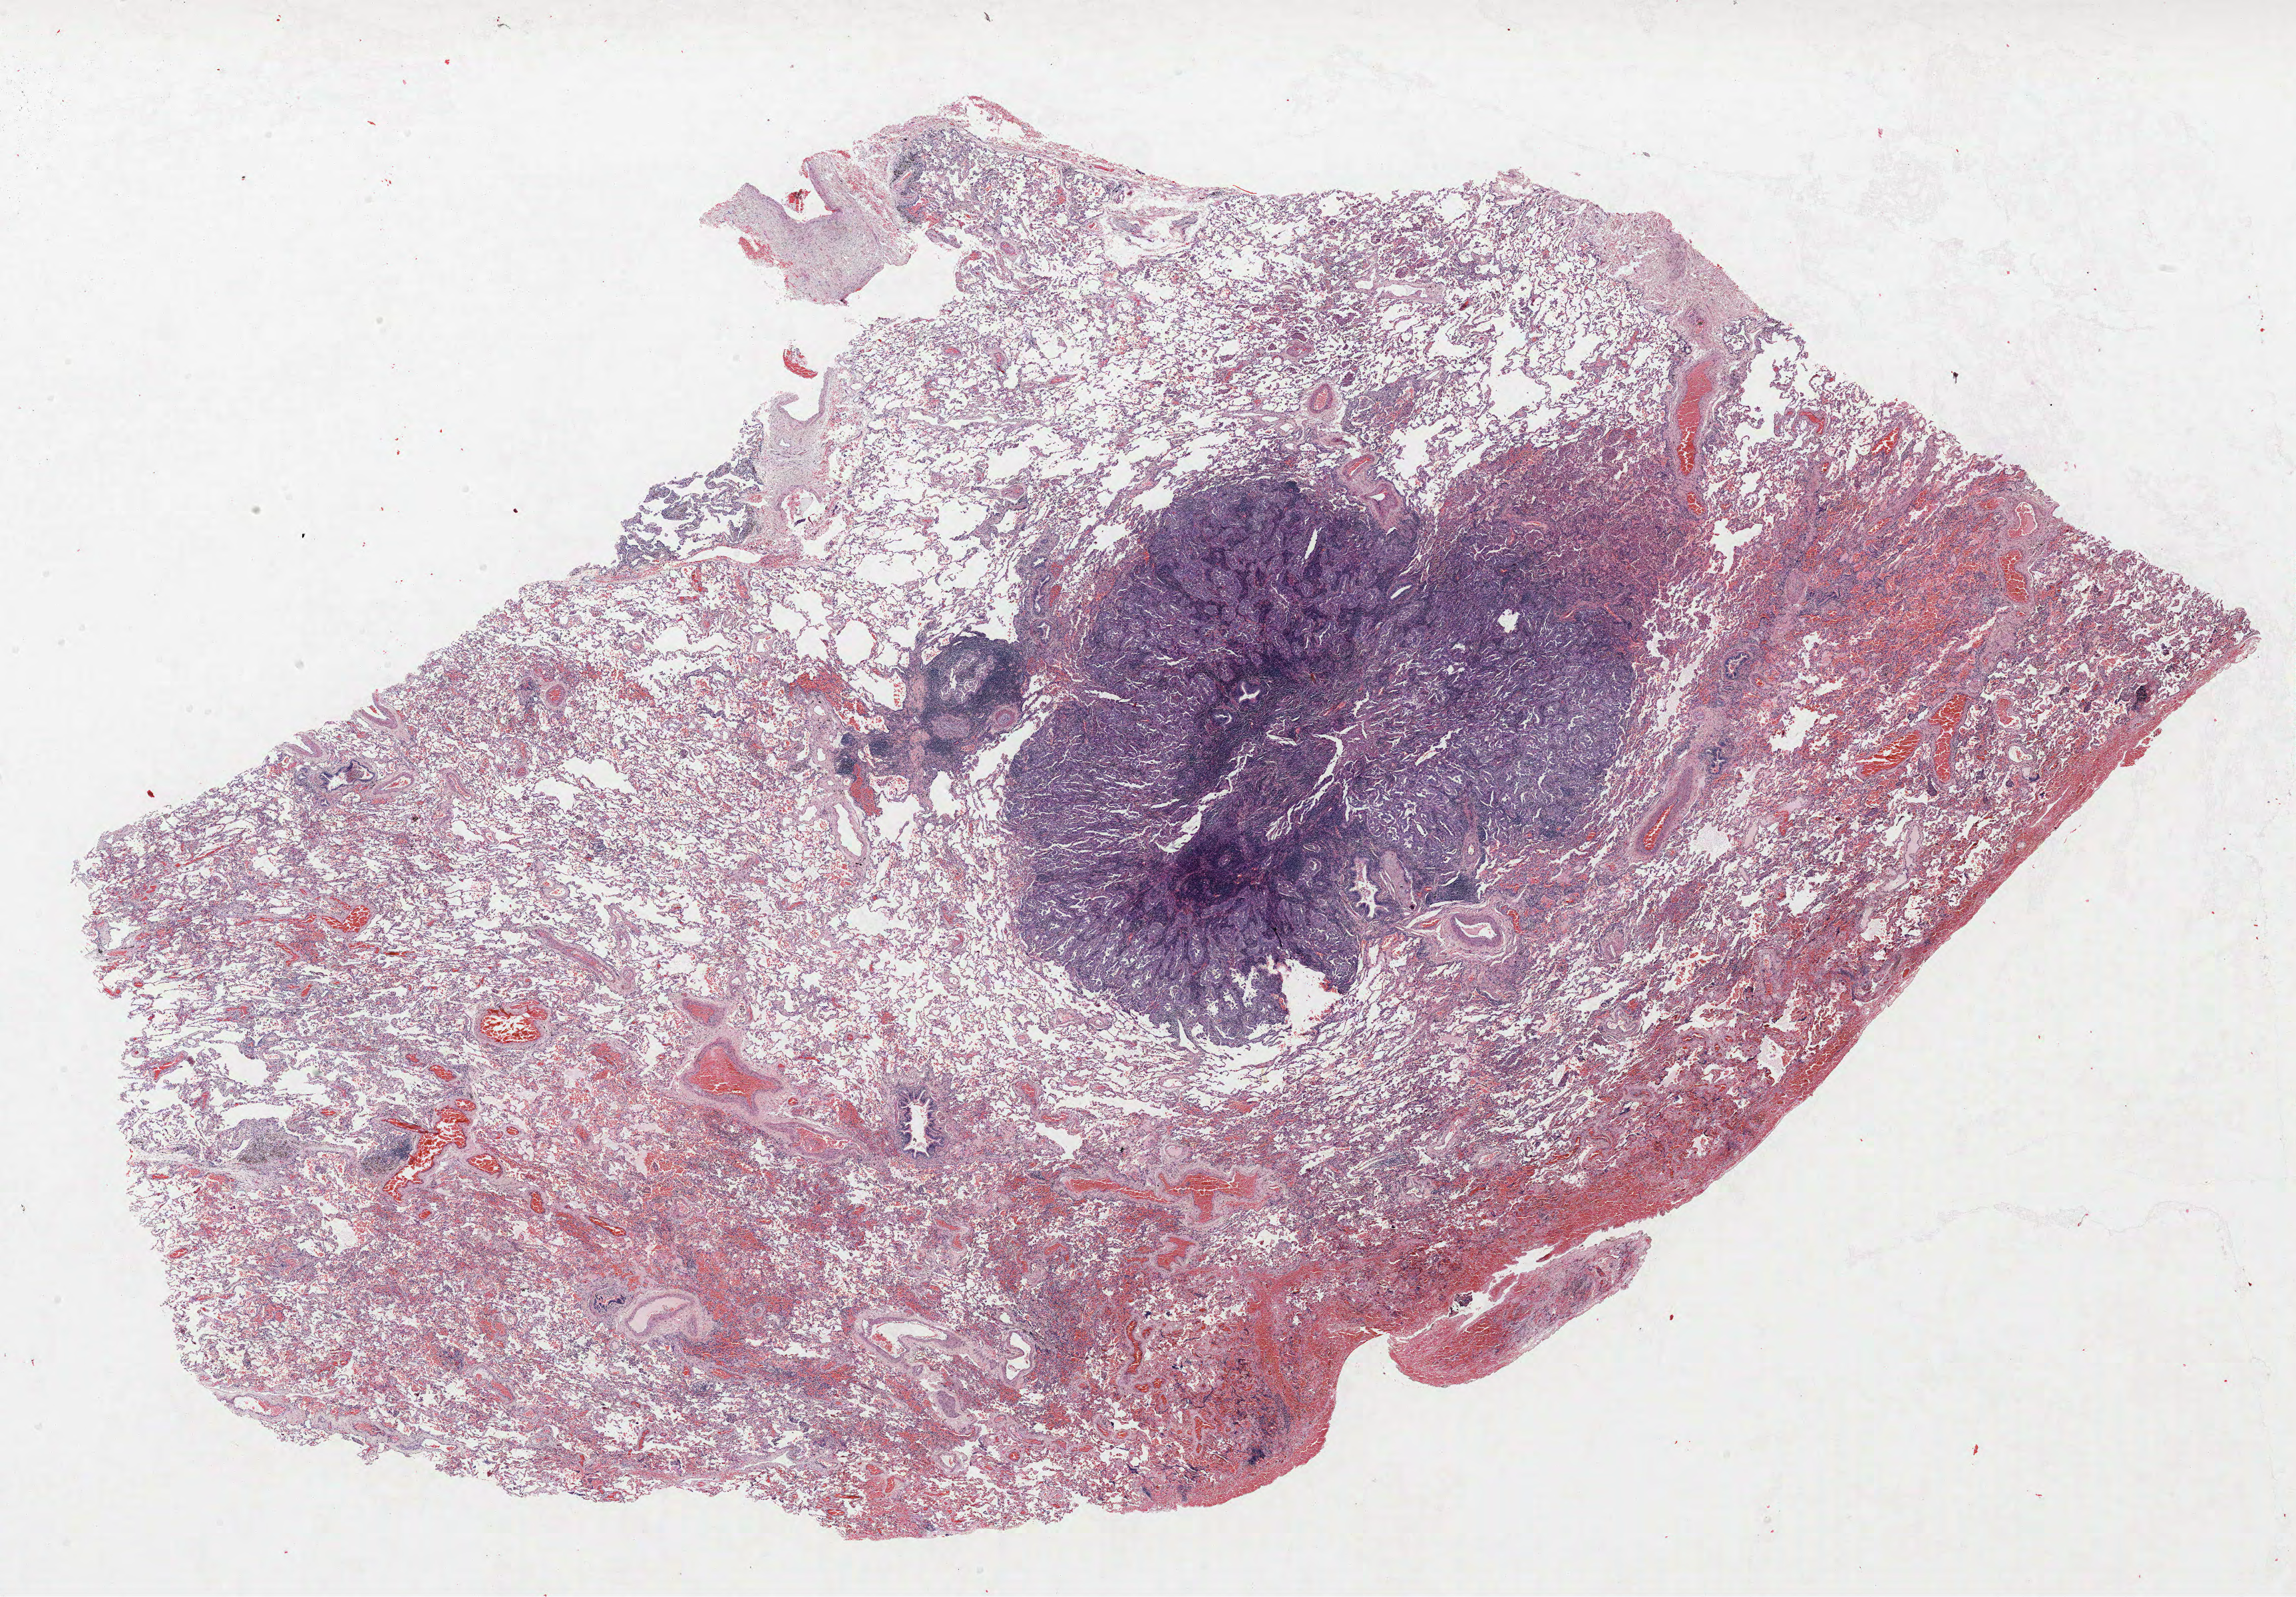
Whole-slide histology image, Hematoxylin and eosin (H&E) stained — shown as a low-resolution overview of the whole scanned area (about 27.6 x 19.2 mm, slide scanned at 40x), FFPE section, lung tissue. Female, age 55 at enrolment. Current smoker at enrolment. Grade: well differentiated (G1).
Primary tumour location (clinical record): left lower lobe. Participant's lung-cancer diagnosis: Adenocarcinoma, NOS (ICD-O-3 8140/3). Tumour size (pathology): 11 mm. Stage (AJCC 6th edition): IA.